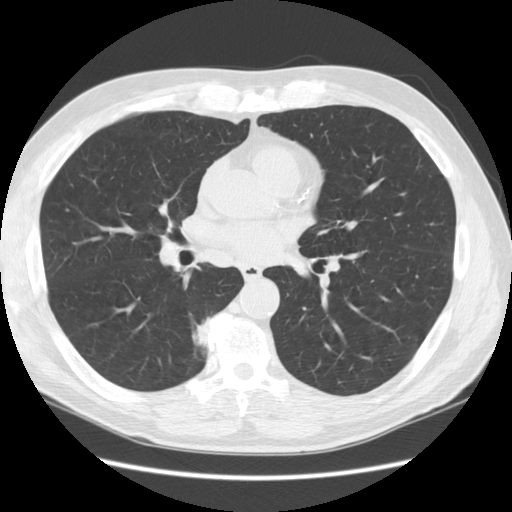
Low-dose screening chest CT, one axial slice. Position 67 of 133 along the scan axis. 120 kVp. Lung window (W 1500 / L -600 HU). 512 × 512 image matrix, field of view 370 × 370 mm.
Outlined on this slice (manually delineated by an expert):
- lesion 1 (tumor, lower lobe of right lung): box from (x=193, y=317) to (x=211, y=346) px